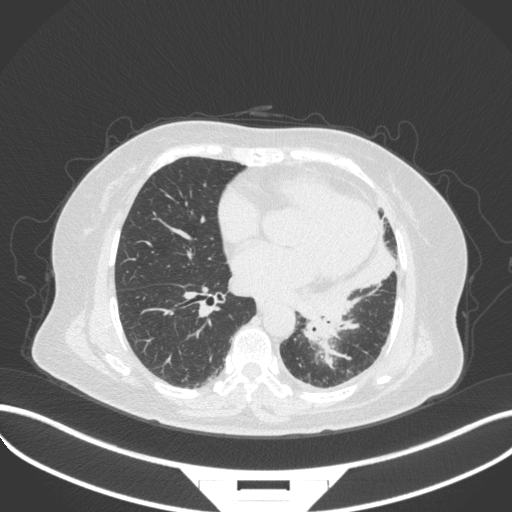
Chest CT, one axial slice. Position 150 of 328 along the scan axis. Reconstruction kernel B31f. 120 kVp. Lung window (W 1500 / L -600 HU). 512 × 512 image matrix, field of view 400 × 400 mm. Female patient, age 69 years. Case-level facts recorded for this patient, not image findings: clinical TNM (as recorded): T2b N3 M1.
Structures marked on this image (rectangle marked by the reading radiologist):
- lung tumour (recorded histology: adenocarcinoma): bounding box [x1, y1, x2, y2] px = [294, 311, 355, 367]